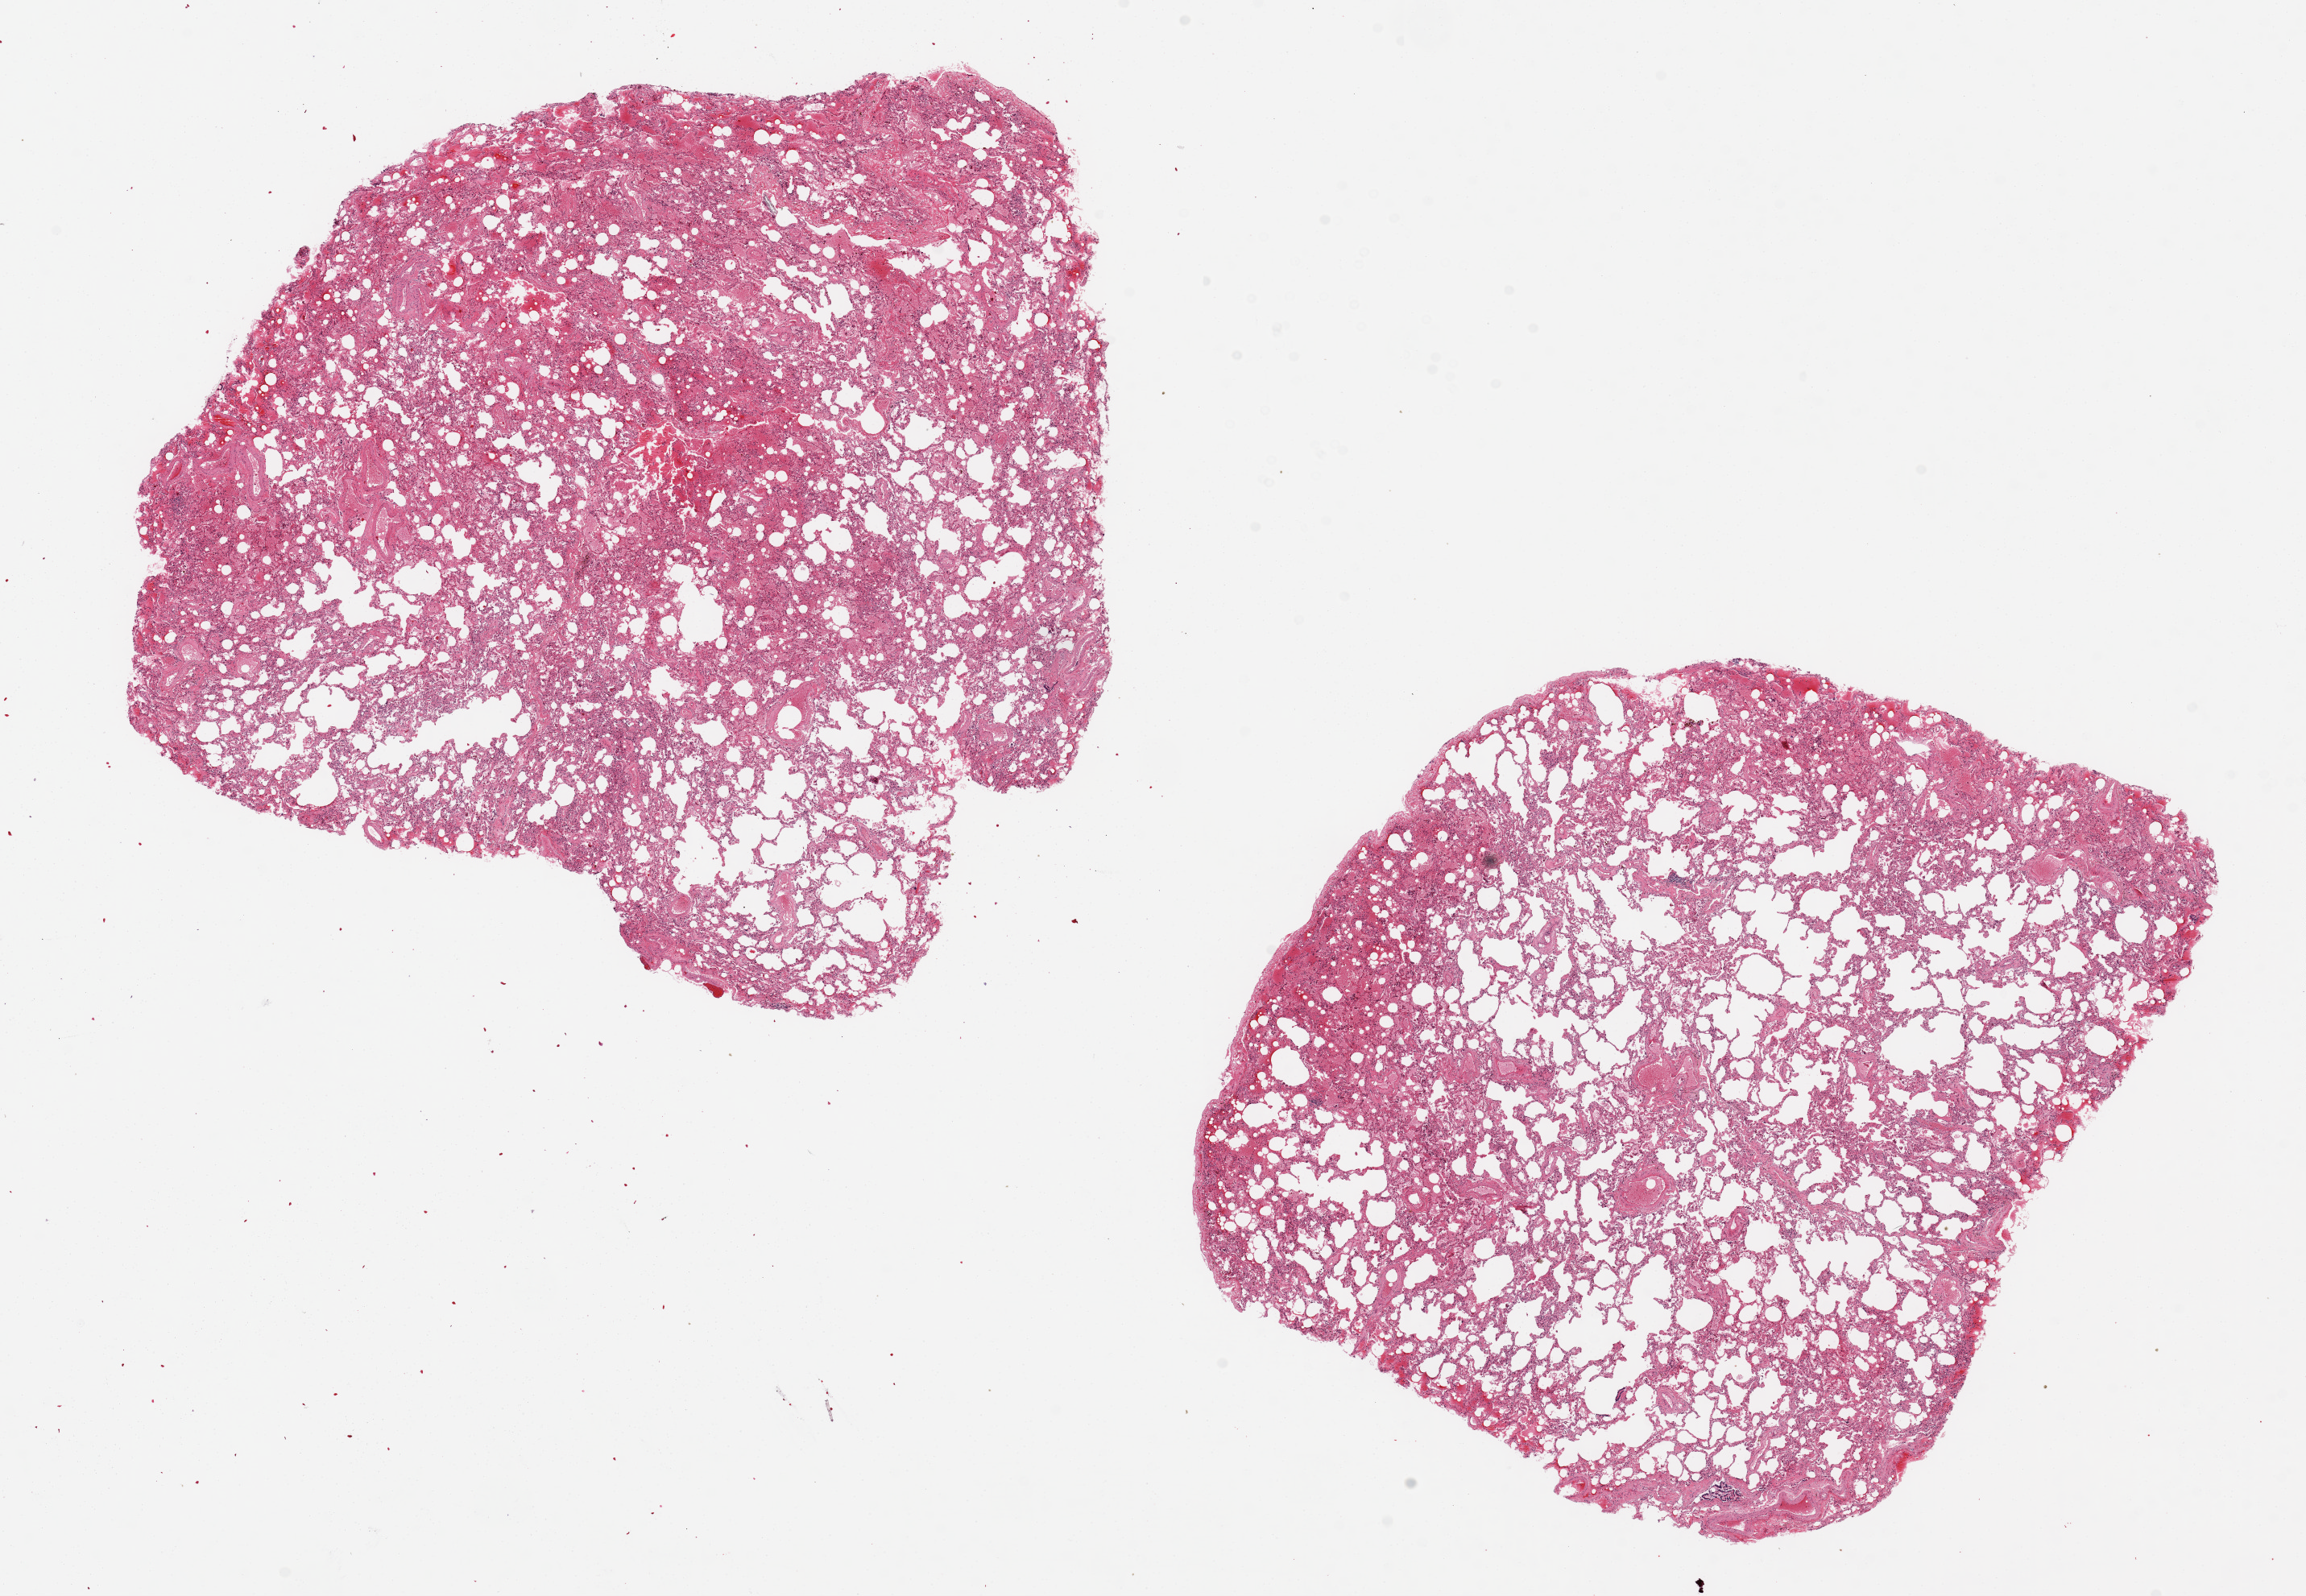
Digitized haematoxylin and eosin-stained section — shown as a low-resolution overview of the whole scanned area (about 22.6 x 15.7 mm, acquisition: 20x scan). PAXgene-fixed paraffin-embedded (PFPE) section. Target tissue: lung. Tissue donor sample. Donor: female.
- pathologist's review note for this sample: 2 ~ 10.5x8.5 aliquots. Bronchiolar mucosa largely sloughed; moderate-alveolar congestion